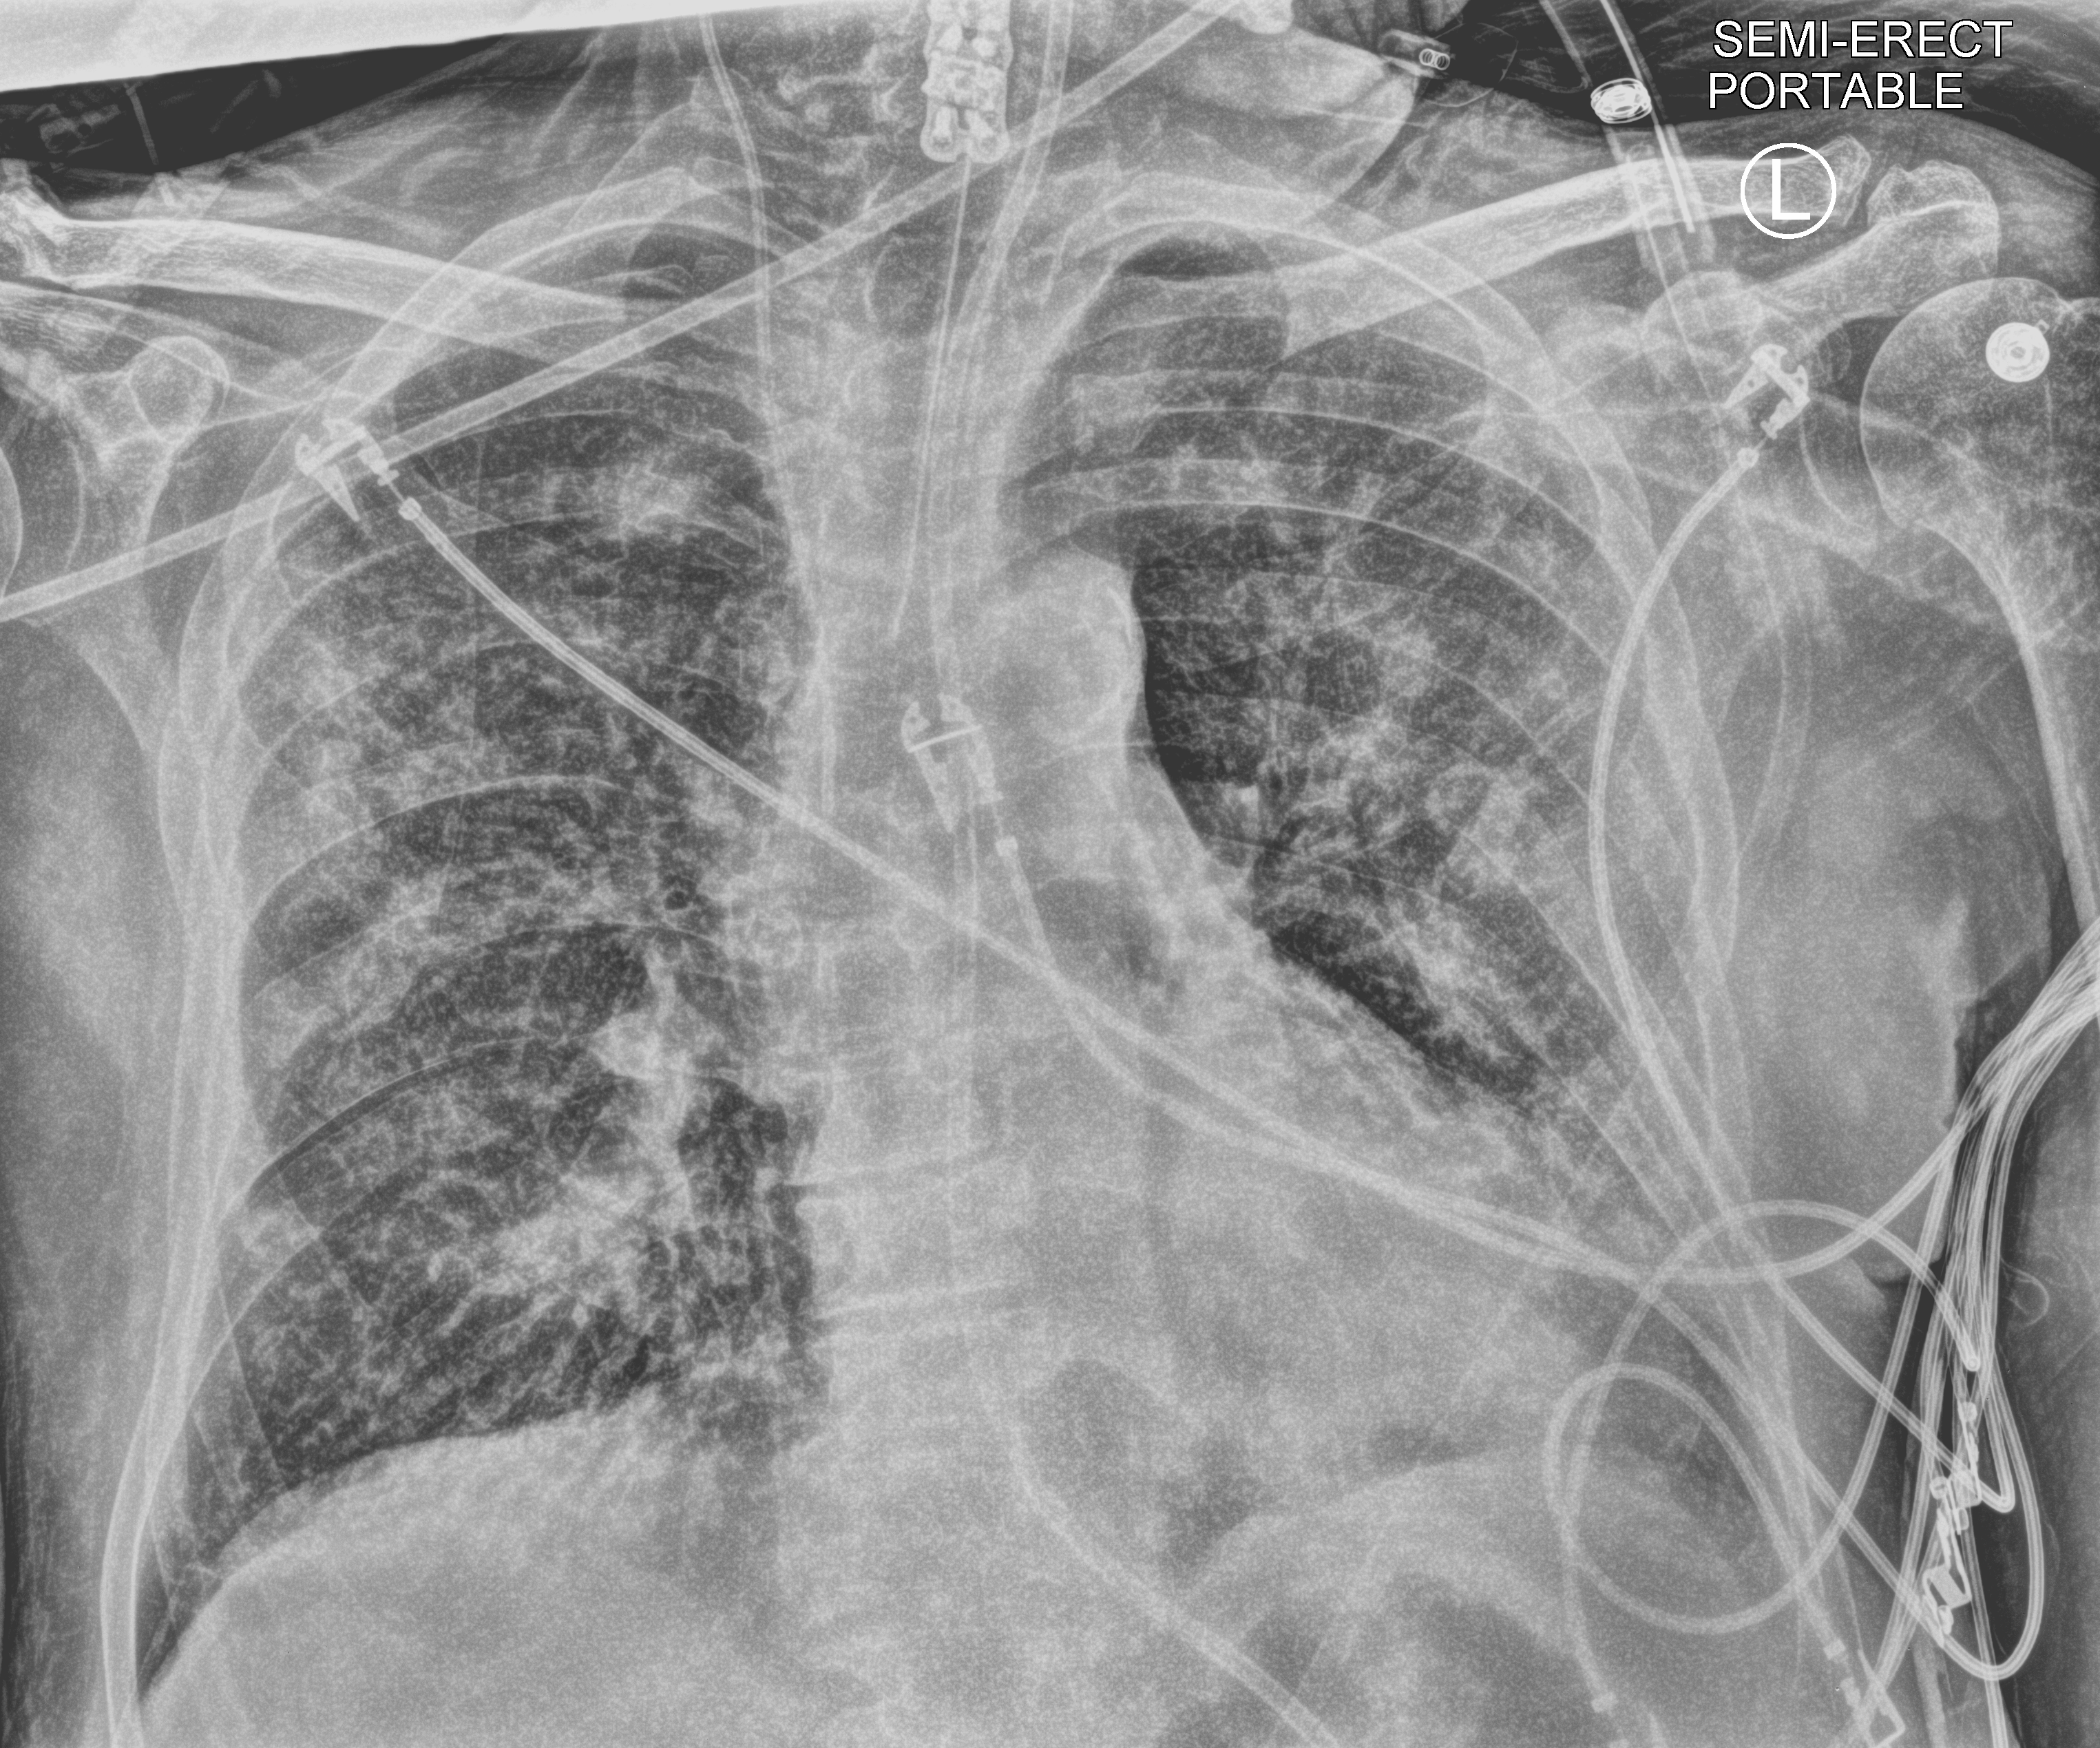
Chest X-ray (portable), anteroposterior (AP) projection. Male patient hospitalised with COVID-19, age 75–90 years.
Hospital-stay facts (about this admission, not read from this image; timing relative to this image not recorded): length of hospital stay: 26 days; diabetes (admission record): no; smoking status (admission record): former.